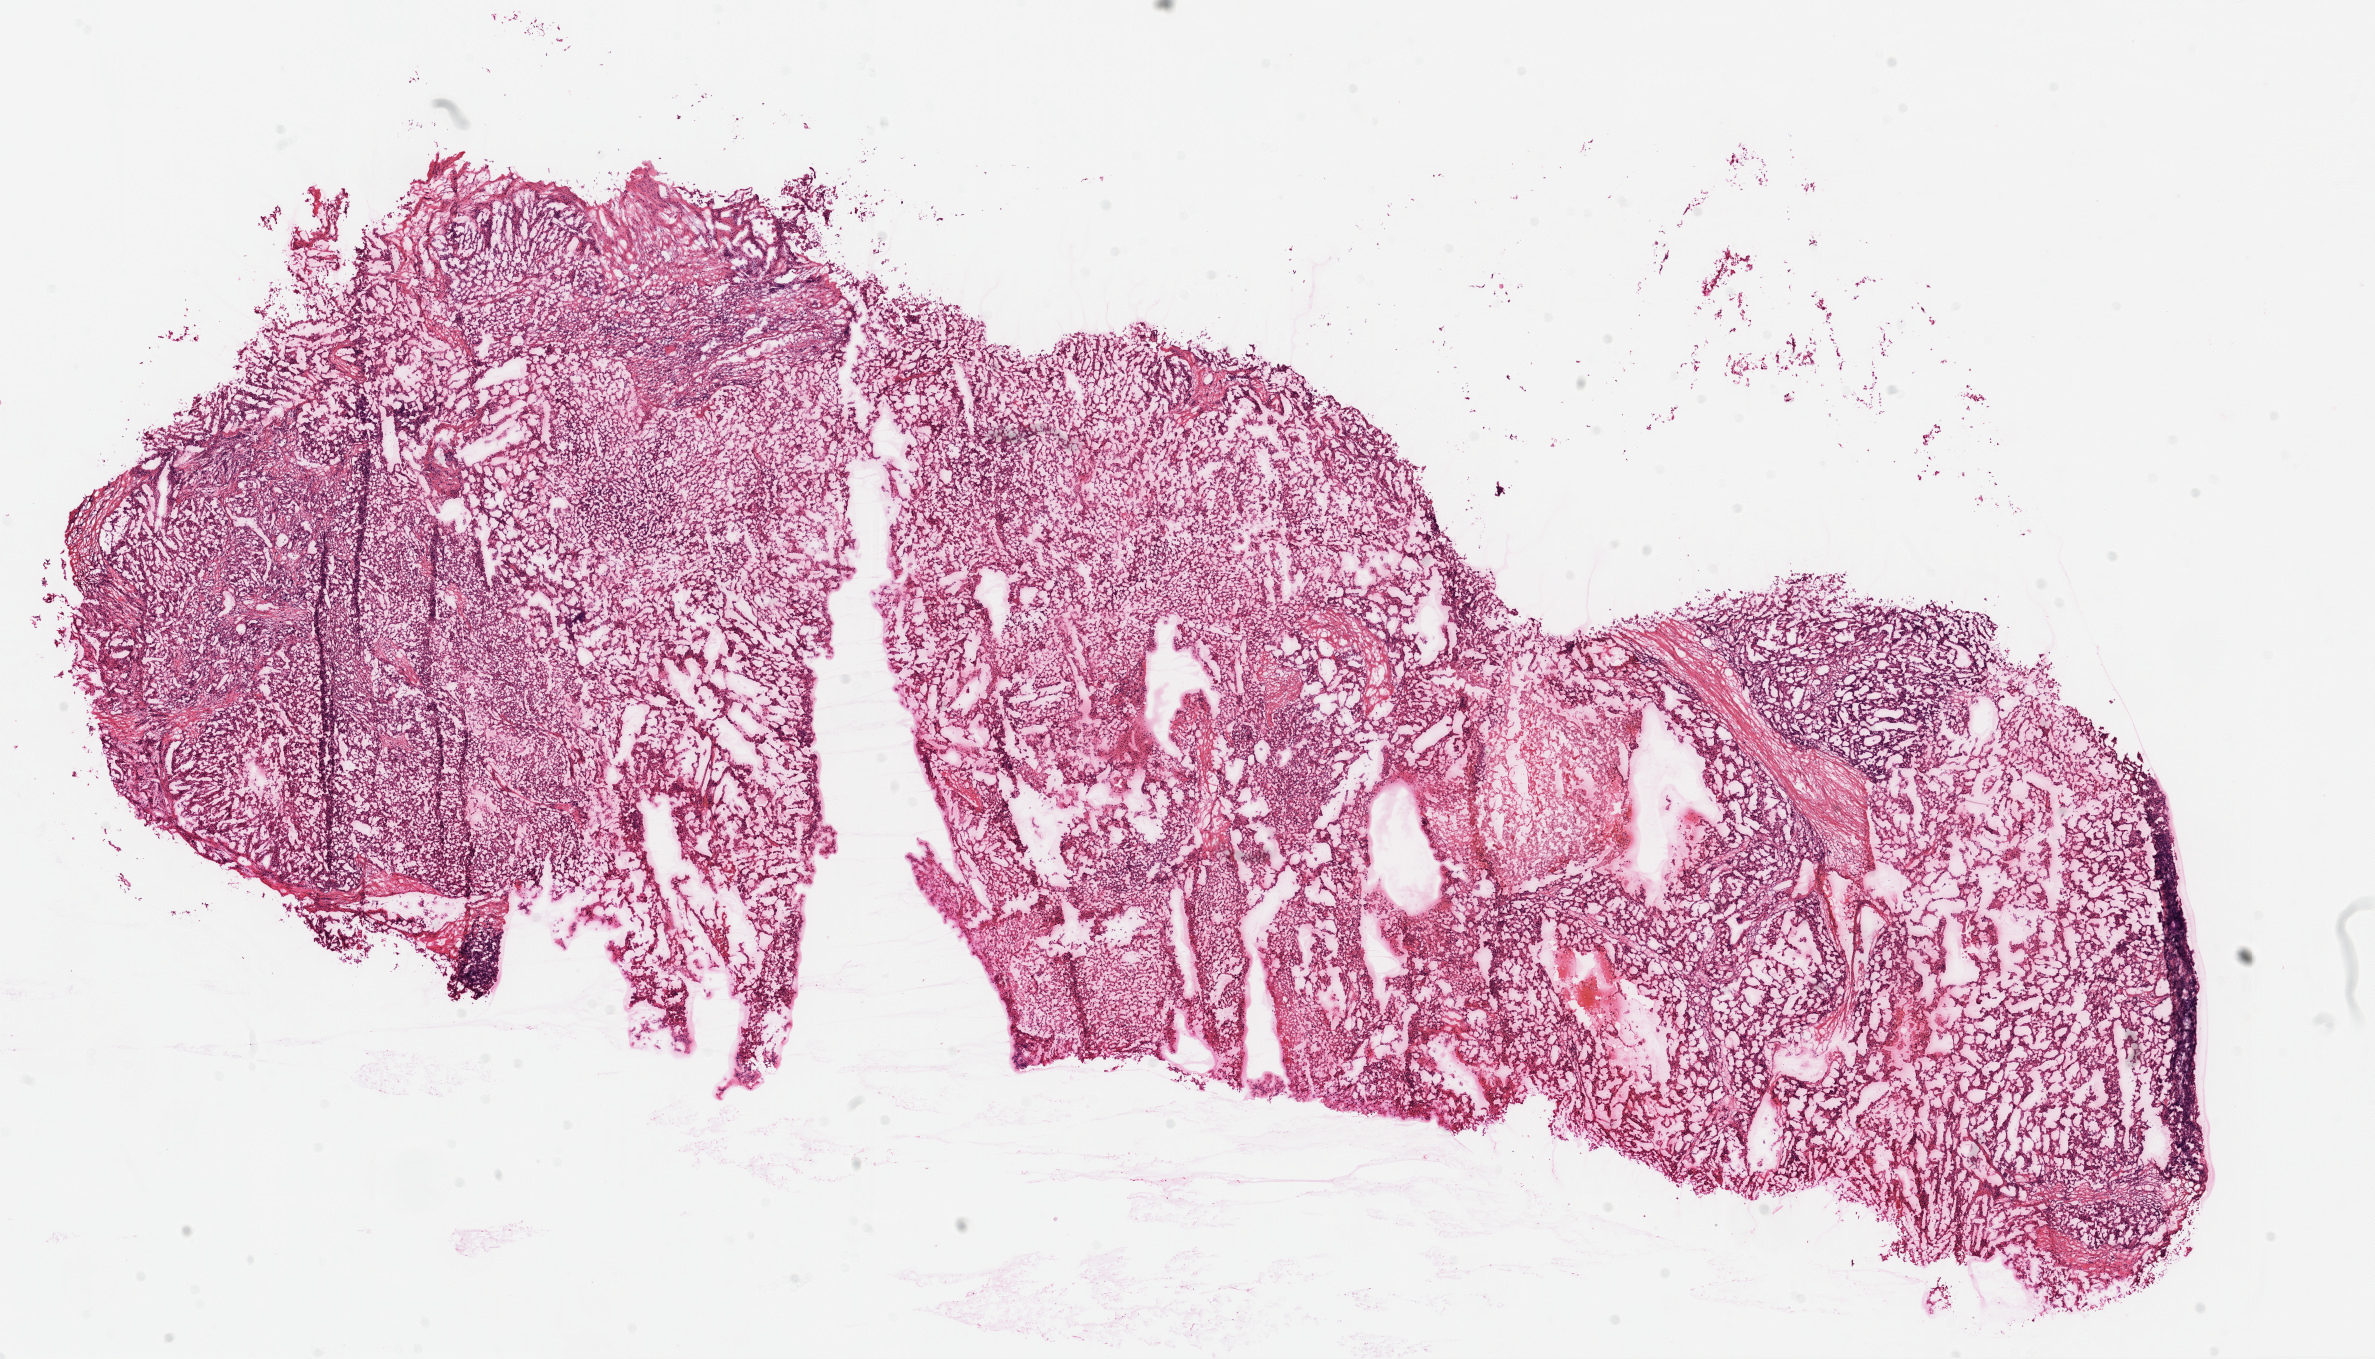
Whole-slide histology image, Hematoxylin and eosin (H&E) stained — a low-resolution overview of the entire scanned area, about 19.1 x 10.9 mm. Frozen section. Kidney, primary tumour sample. Patient: female, age at initial diagnosis 46 years. Histologic grade: G4 (undifferentiated). Pathologist review of this section (percent, as recorded): tumour cells 92%, tumour nuclei 80%, normal cells 0%, stromal cells 5%, necrosis 3%.
Pathologic diagnosis: Clear cell adenocarcinoma, NOS. AJCC pathologic stage: IV. Laterality: left.